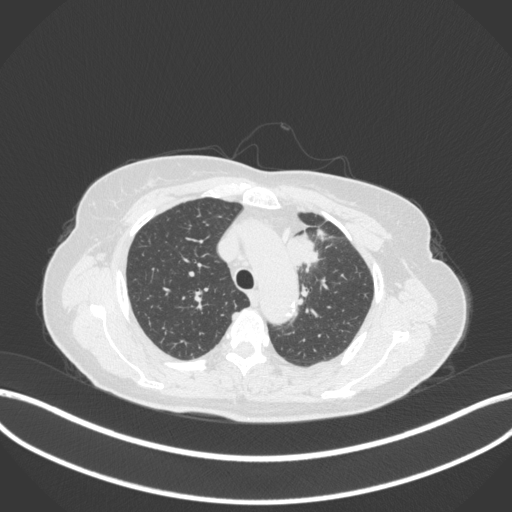
Chest CT, one axial slice. Position 252 of 368 along the scan axis. 120 kVp. Lung window (W 1500 / L -600 HU). 1 mm slice thickness. 512 × 512 image matrix, field of view 400 × 400 mm. Female patient, age 65 years. From the clinical record (not read from this slice): clinical TNM (as recorded): T2a N0 M0; histopathological grade: G2-3.
Outlined on this slice (bounding box drawn by a radiologist):
- lung tumour (recorded histology: adenocarcinoma): bounding box <284,229,321,272> (left, top, right, bottom; pixels)